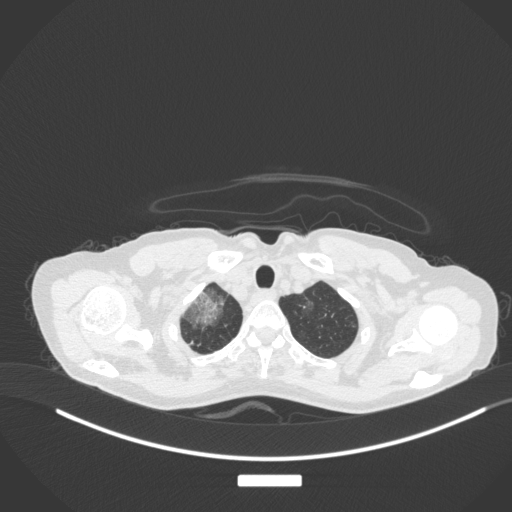
Chest CT, one axial slice; position 301 of 311 along the scan axis; lung window (W 1500 / L -600 HU); 1 mm slice thickness; 512 × 512 image matrix. Patient: female, 59 years. Case-level facts recorded for this patient, not image findings: clinical TNM (as recorded): T3 N0 M0.
Annotated regions visible in this slice (bounding box drawn by a radiologist):
- lung tumour (recorded histology: adenocarcinoma): box from (x=179, y=289) to (x=225, y=333) px